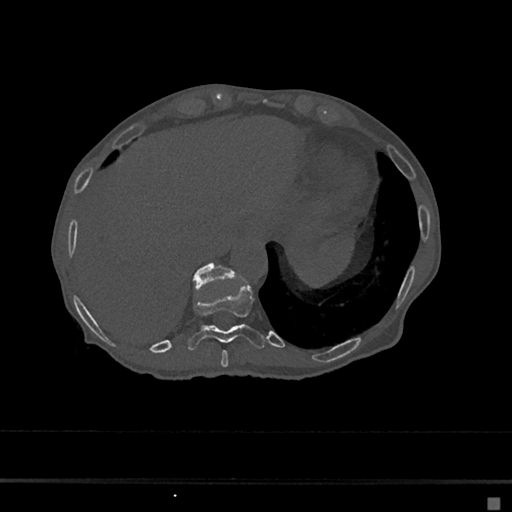
CT including the spine, one axial slice; slice 221 of 797 in the series (ordered by position); reconstruction kernel Br40s/3; bone window (W 1800 / L 400 HU); 0.5 mm slice thickness; 512 × 512 image matrix. Patient: female, 68 years. Case-level facts recorded for this patient, not image findings: primary cancer: renal.
Outlined on this slice (semi-automatically segmented with operator editing):
- T10 vertebra: bounding box [x1, y1, x2, y2] px = [188, 284, 265, 351]
- T11 vertebra: [192, 263, 235, 291]
- T9 vertebra: [220, 350, 229, 367]